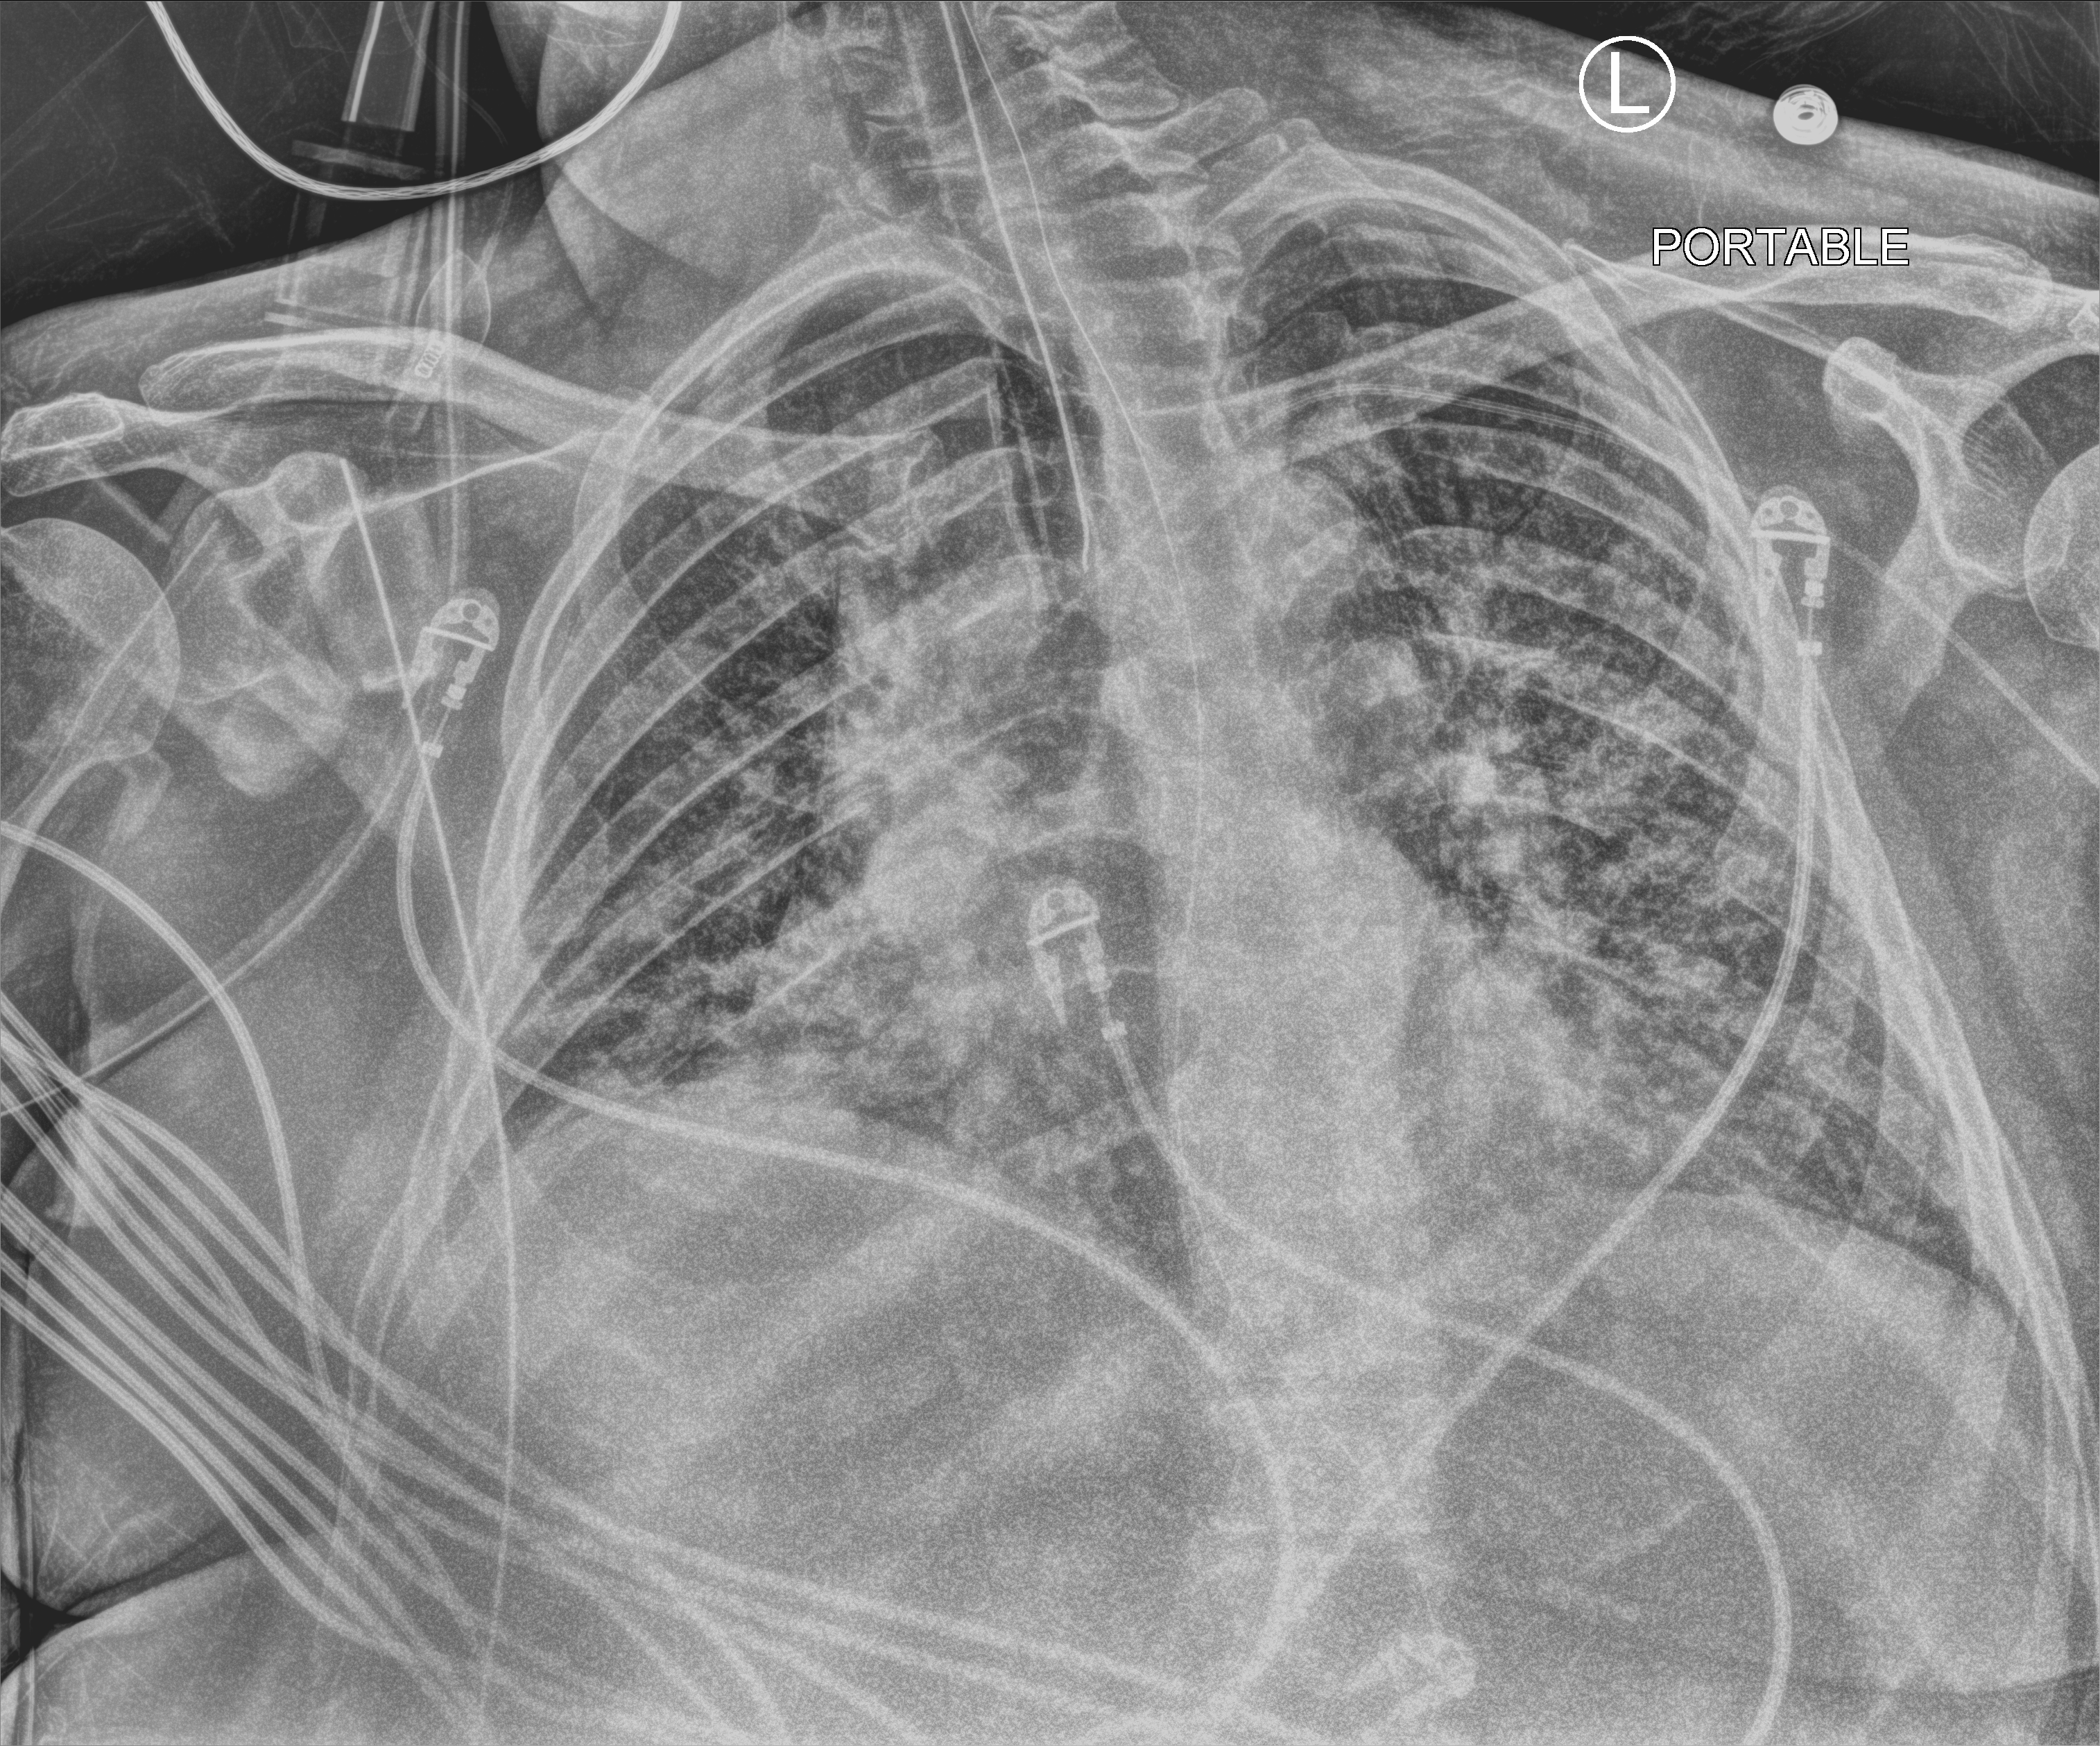
Chest X-ray (portable); anteroposterior (AP) projection. Male patient hospitalised with COVID-19, age 18–59 years.
Hospital-stay facts (about this admission, not read from this image; timing relative to this image not recorded): hypertension (admission record): yes; other chronic lung disease (admission record): no.